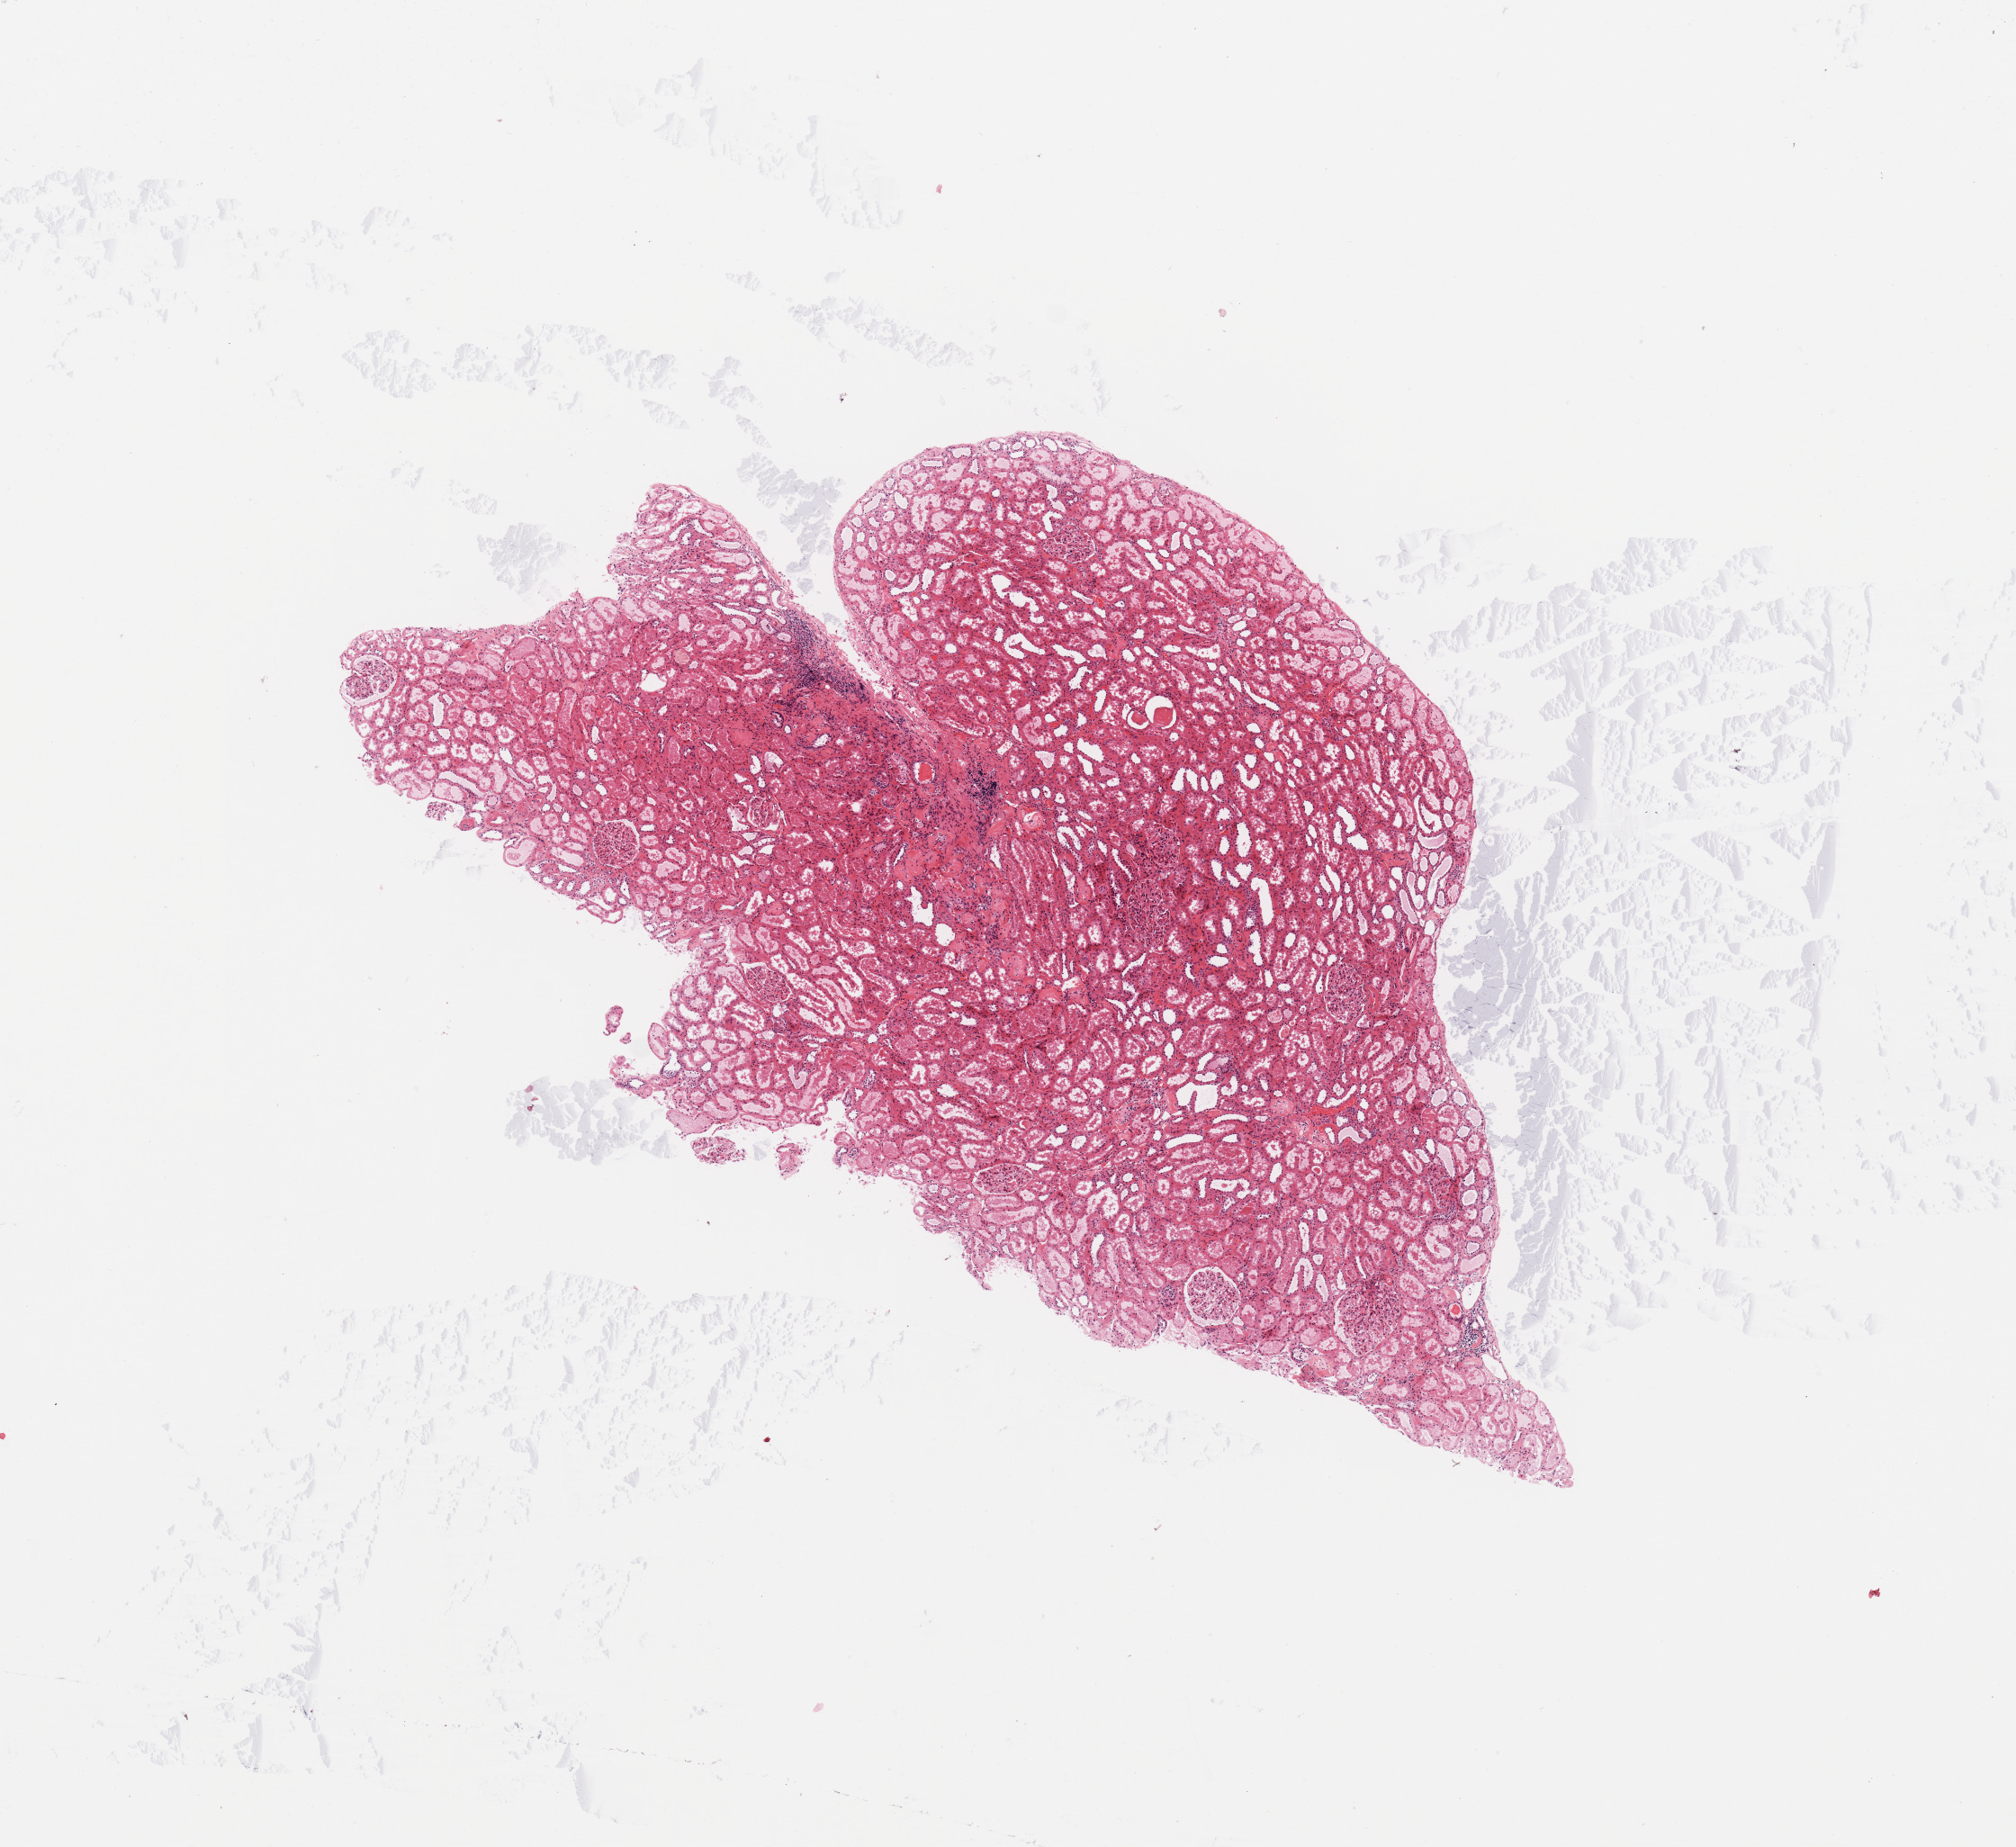
Digitized H&E tissue section (whole slide) — shown as a low-resolution overview of the whole scanned area (about 8.9 x 8.1 mm, slide scanned at 20x). Normal (non-tumour) tissue sample, kidney. Male, 63 y/o.
This section: normal (non-tumour) tissue from the same patient. Patient diagnosis: Renal cell carcinoma, NOS.